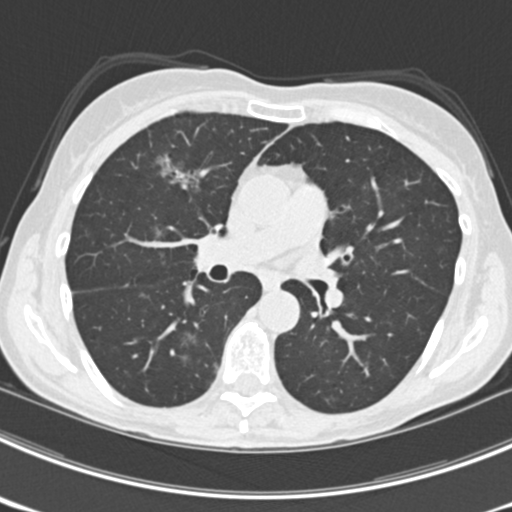
Axial slice from a low-dose chest CT screening exam, third annual screen, lung window (W 1500 / L -600 HU), 2 mm slice thickness, standard (soft-tissue) reconstruction kernel (B30f), 120 kVp, slice 91 of 225 in the series, 512 × 512 image matrix, field of view 302 × 302 mm. Female, age 63 years at enrolment.
• Expert reader's lesion annotation, bounding box [x1, y1, x2, y2] px = [151, 142, 215, 200].
• The screening reader recorded 9 non-calcified nodules or masses ≥4 mm on this exam; which of them this box marks is not recorded.